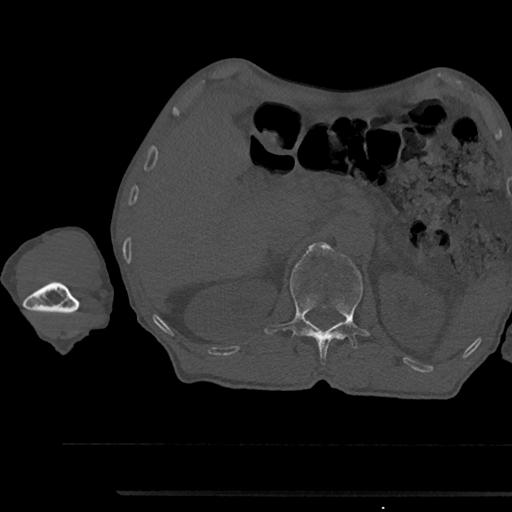
CT including the spine, one axial slice. Position 641 of 797 along the scan axis. Reconstruction kernel Br40s/3. 120 kVp. Bone window (W 1800 / L 400 HU). 0.5 mm slice thickness. 512 × 512 image matrix, field of view 367 × 367 mm. Patient: male, 79 years. Case-level facts recorded for this patient, not image findings: primary cancer: prostate.
Structures marked on this image (semi-automatic segmentation, software-assisted and operator-edited):
- L1 vertebra: bounding box <265,242,368,361> (left, top, right, bottom; pixels)